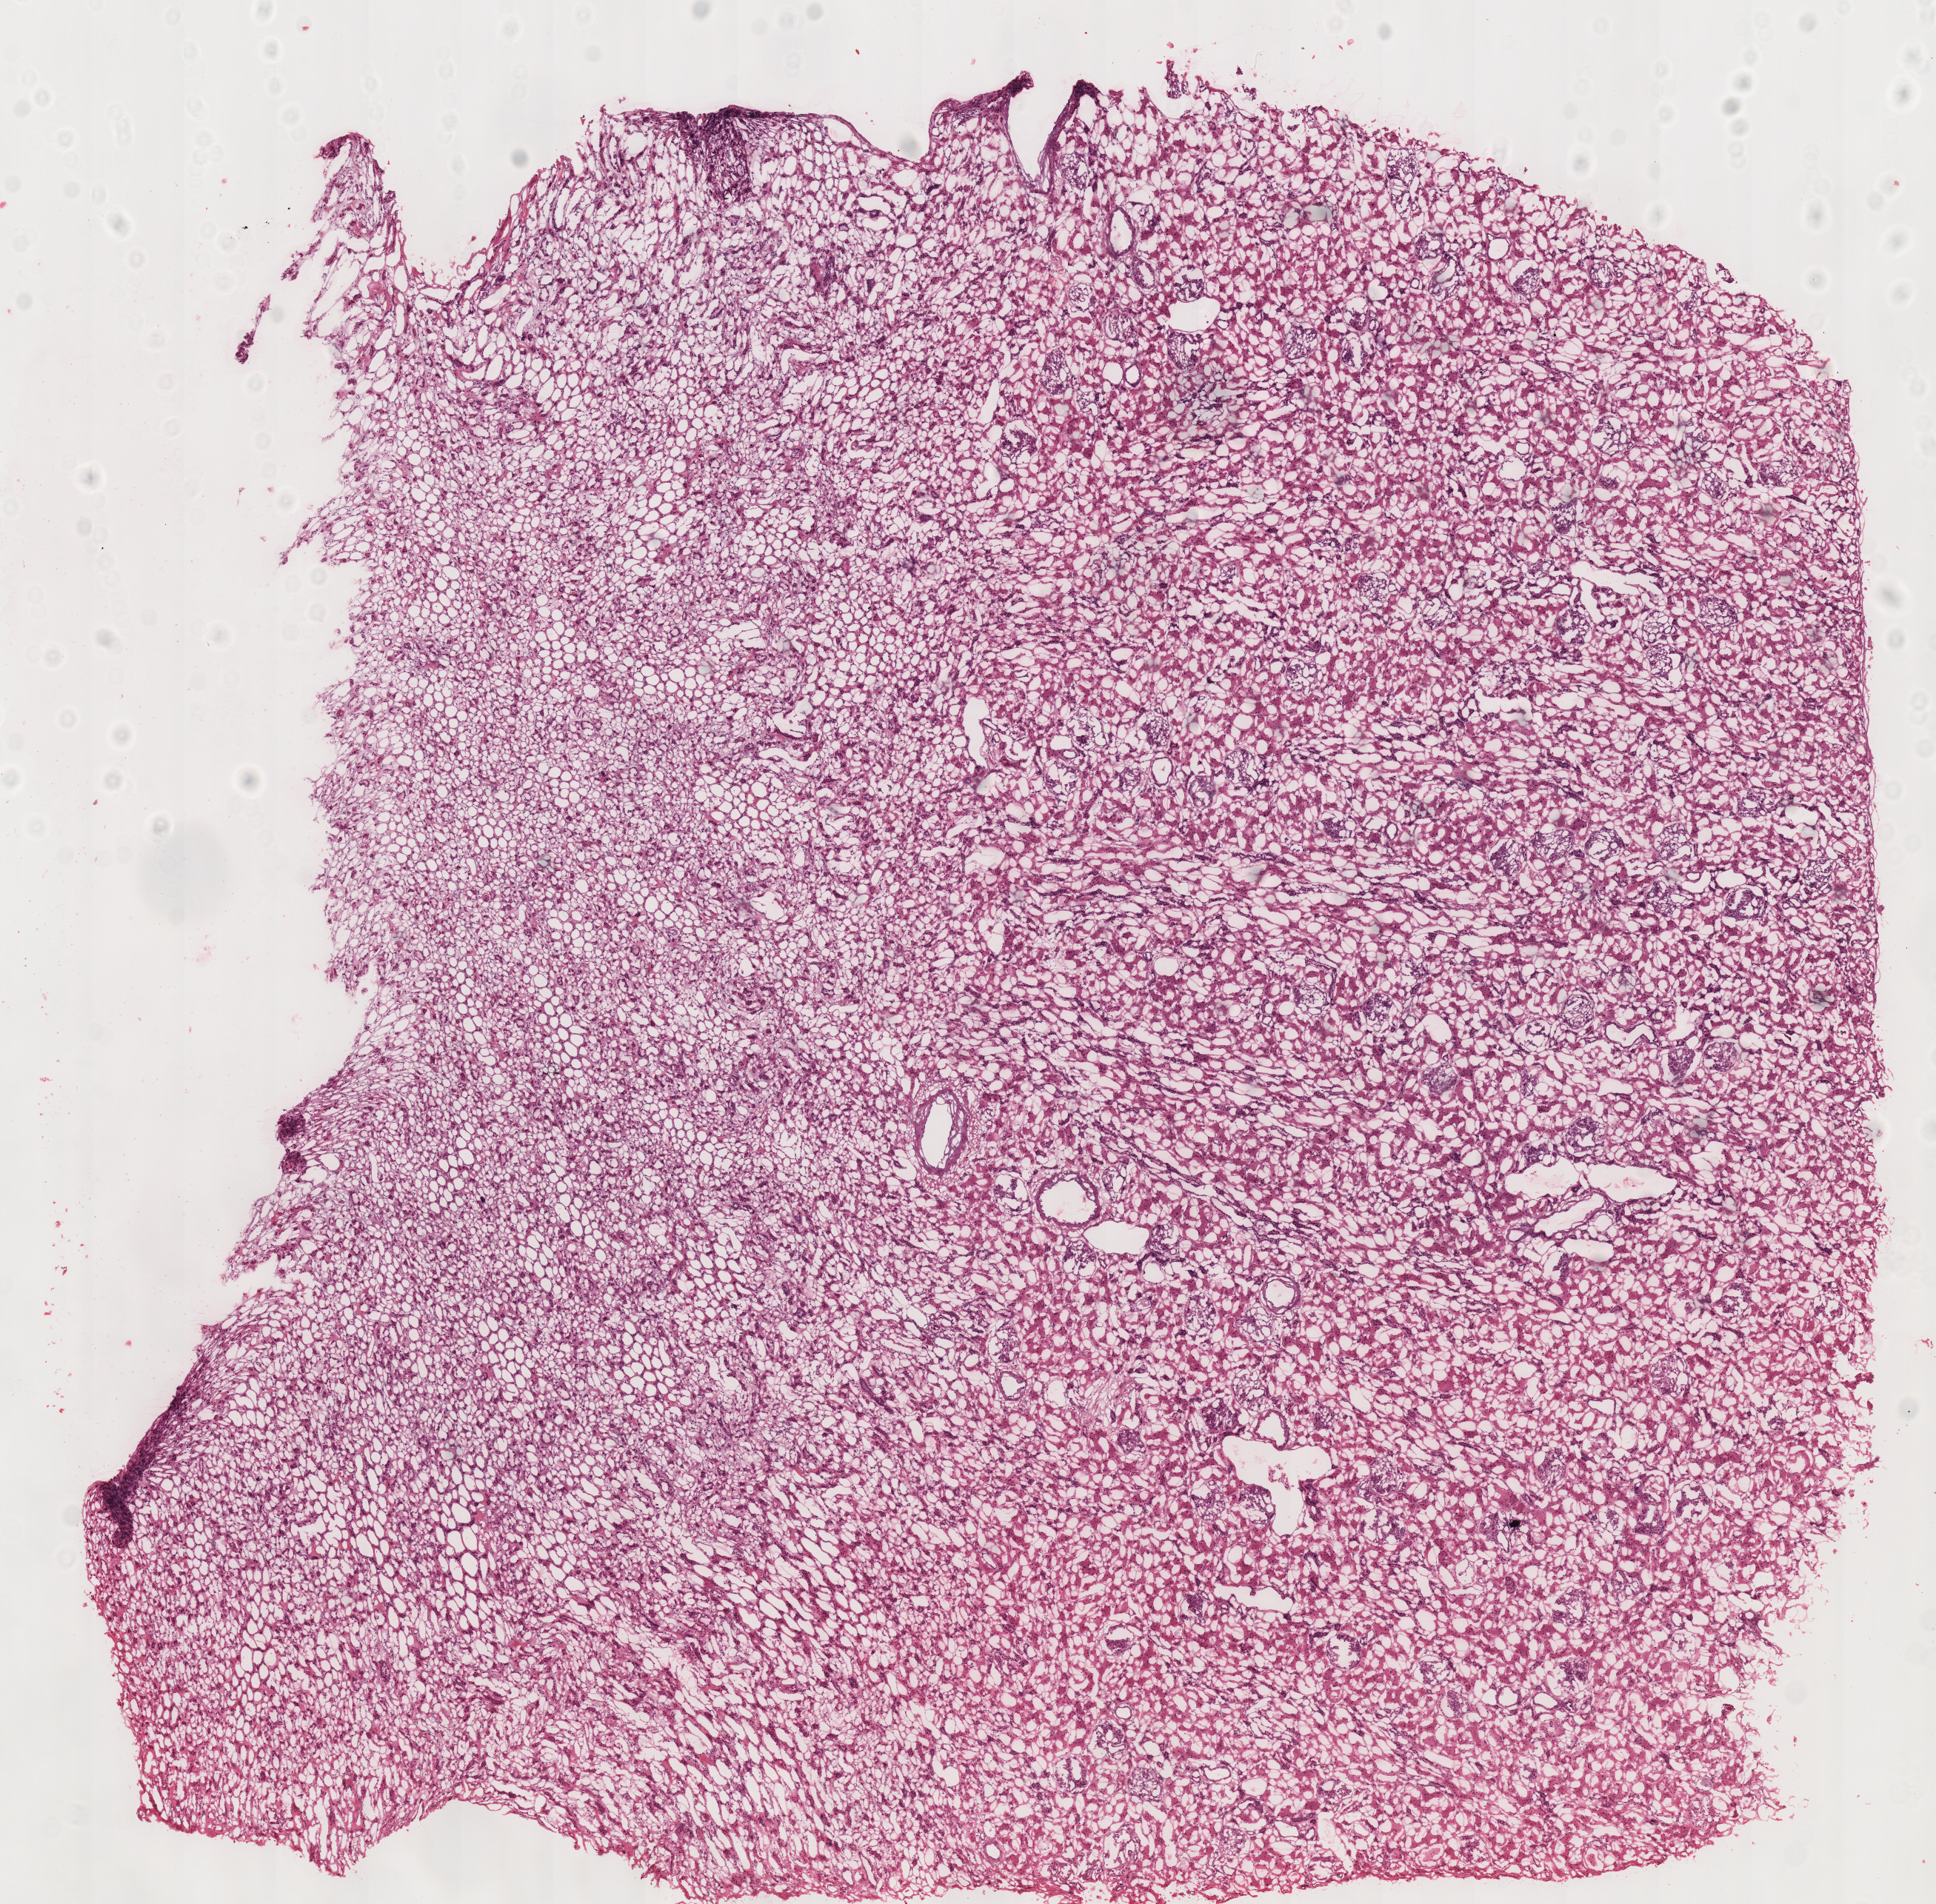
Digitized Hematoxylin and eosin (H&E) stained tissue section (whole slide) — low-resolution overview of the scanned area, about 10.3 x 10.1 mm (acquisition: 40x scan). Frozen section from the top of the tissue portion. Kidney, solid tissue normal (non-tumour tissue) sample. Female, age 42 years at initial diagnosis. Inflammatory infiltration, as recorded: lymphocyte infiltration 0%, monocyte infiltration 0%, neutrophil infiltration 0%.
- this section: solid tissue normal (non-tumour) sample from the same patient
- patient diagnosis: Renal cell carcinoma, chromophobe type